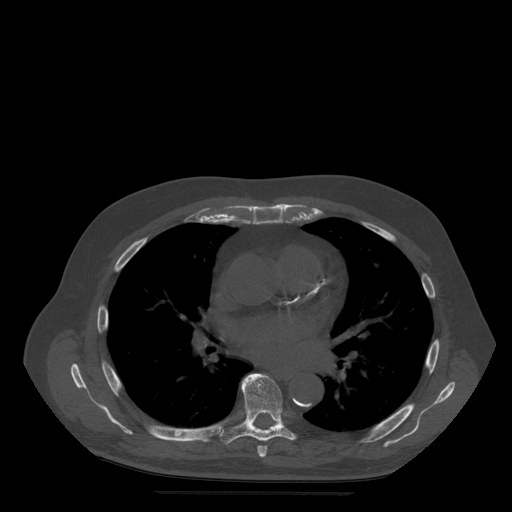
CT including the spine, one axial slice; position 336 of 522 along the scan axis; bone window (W 1800 / L 400 HU); 1.25 mm slice thickness; 512 × 512 image matrix. Patient age 72 years. From the clinical record (not read from this slice): primary cancer: prostate.
Annotated regions visible in this slice (semi-automatic segmentation, software-assisted and operator-edited):
- T6 vertebra: bounding box <243,384,268,458> (left, top, right, bottom; pixels)
- T7 vertebra: <208,374,297,444>